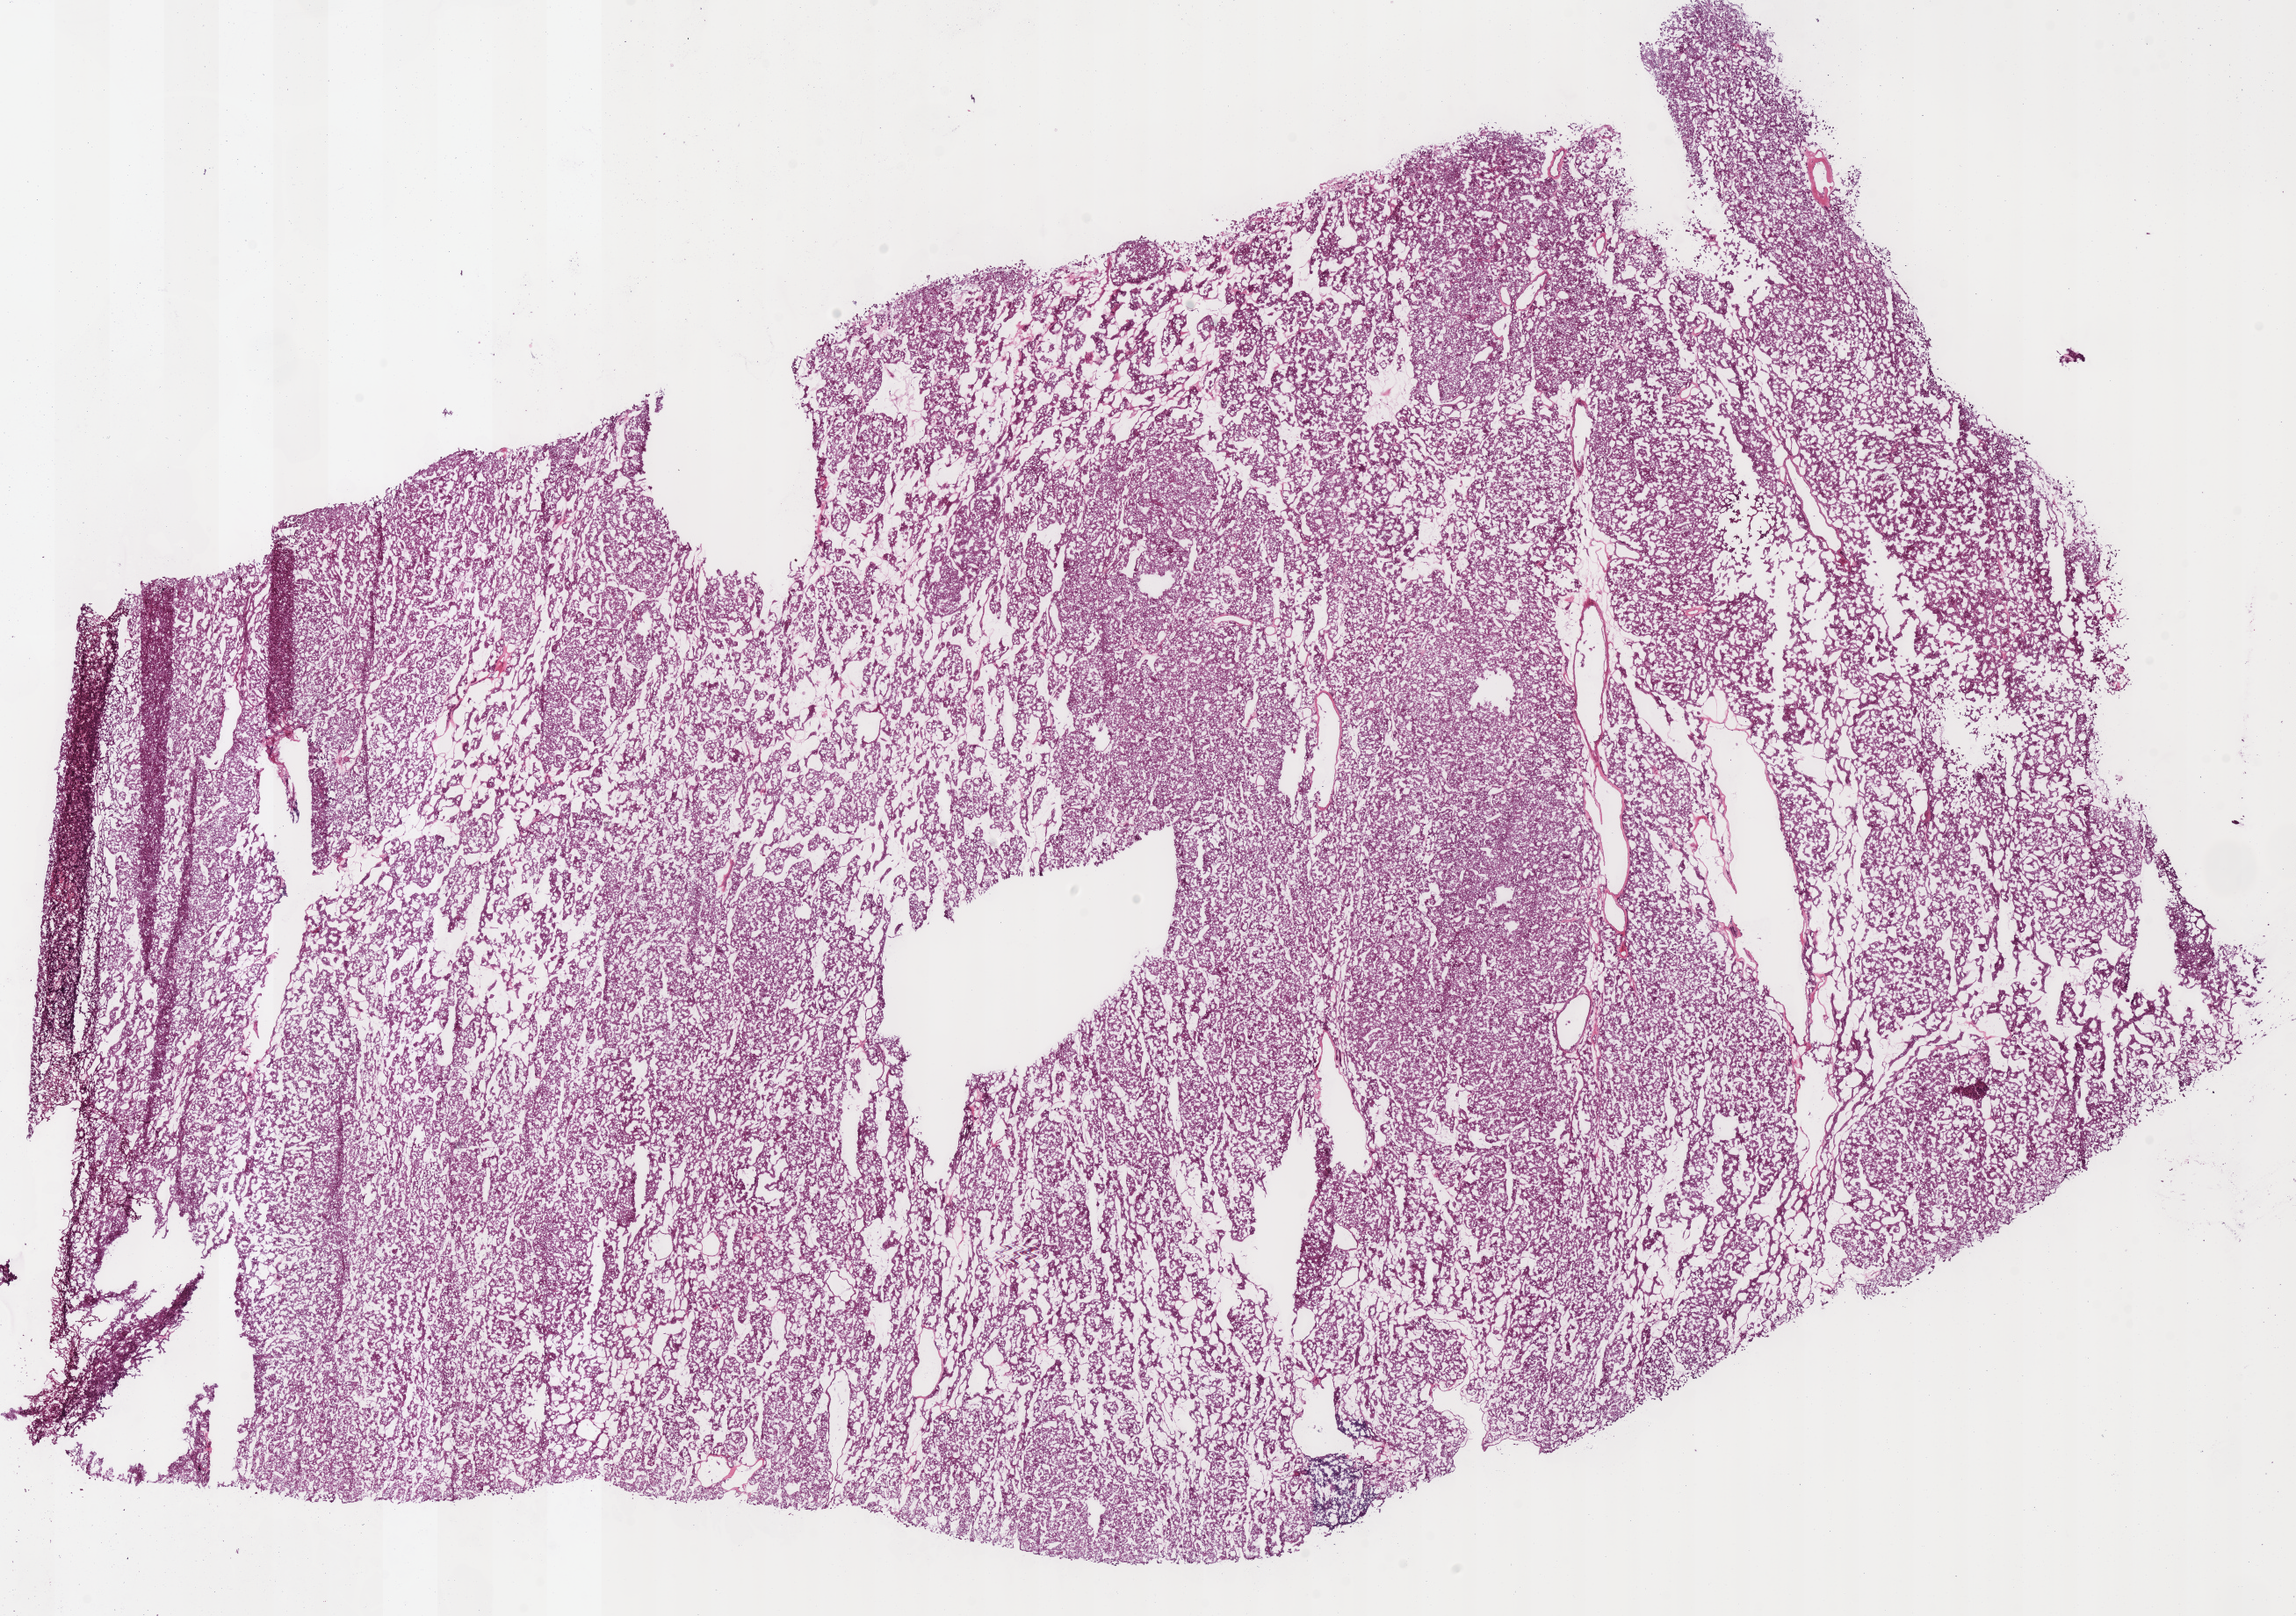
H&E-stained whole-slide image — shown as a low-resolution overview of the whole scanned area (about 20.6 x 14.5 mm, from a 40x scan); frozen section; sample: primary tumour, kidney. Male patient; age at initial diagnosis 69 years. Composition of this section per pathologist review: tumour cells 100%, tumour nuclei 90%.
Pathologic diagnosis: Renal cell carcinoma, chromophobe type.